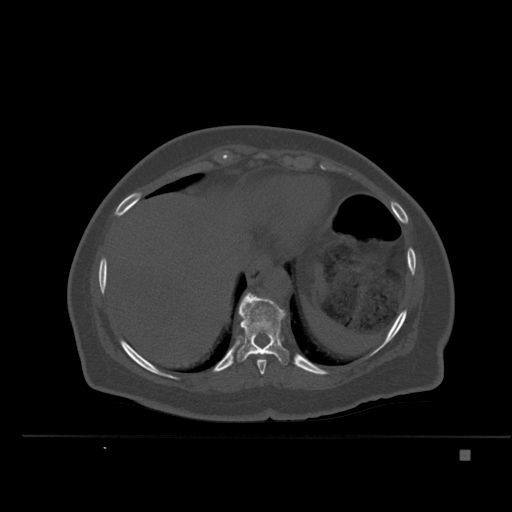
CT including the spine, one axial slice; slice 286 of 477 in the series (ordered by position); bone window (W 1800 / L 400 HU); 1.5 mm slice thickness; 512 × 512 image matrix, field of view 422 × 422 mm. Female patient, age 74 years. From the clinical record (not read from this slice): primary cancer: colon.
Outlined on this slice (semi-automatic segmentation, software-assisted and operator-edited):
- T10 vertebra: box from (x=237, y=293) to (x=289, y=365) px
- T11 vertebra: (x=247, y=292)–(x=249, y=294)
- T9 vertebra: (x=253, y=353)–(x=267, y=375)